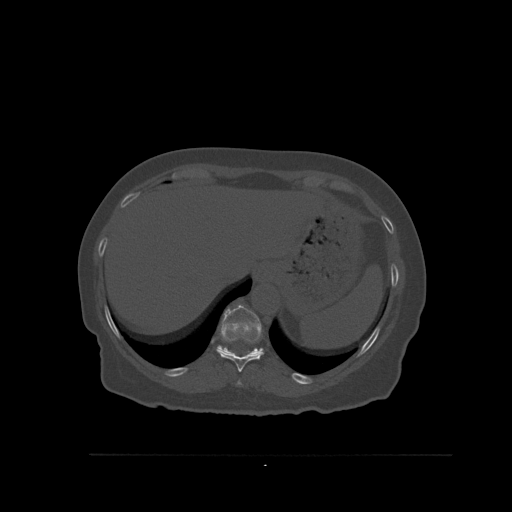
CT including the spine, one axial slice. Slice 315 of 527 in the series (ordered by position). Bone window (W 1800 / L 400 HU). 512 × 512 image matrix. Female patient, age 73 years. Case-level facts recorded for this patient, not image findings: primary cancer: breast; vertebrae with lytic lesions (as recorded): L2.
Annotated regions visible in this slice (semi-automatic segmentation, software-assisted and operator-edited):
- T10 vertebra: bounding box <216,337,264,372> (left, top, right, bottom; pixels)
- T11 vertebra: <217,304,264,357>
- T9 vertebra: <236,380,242,385>